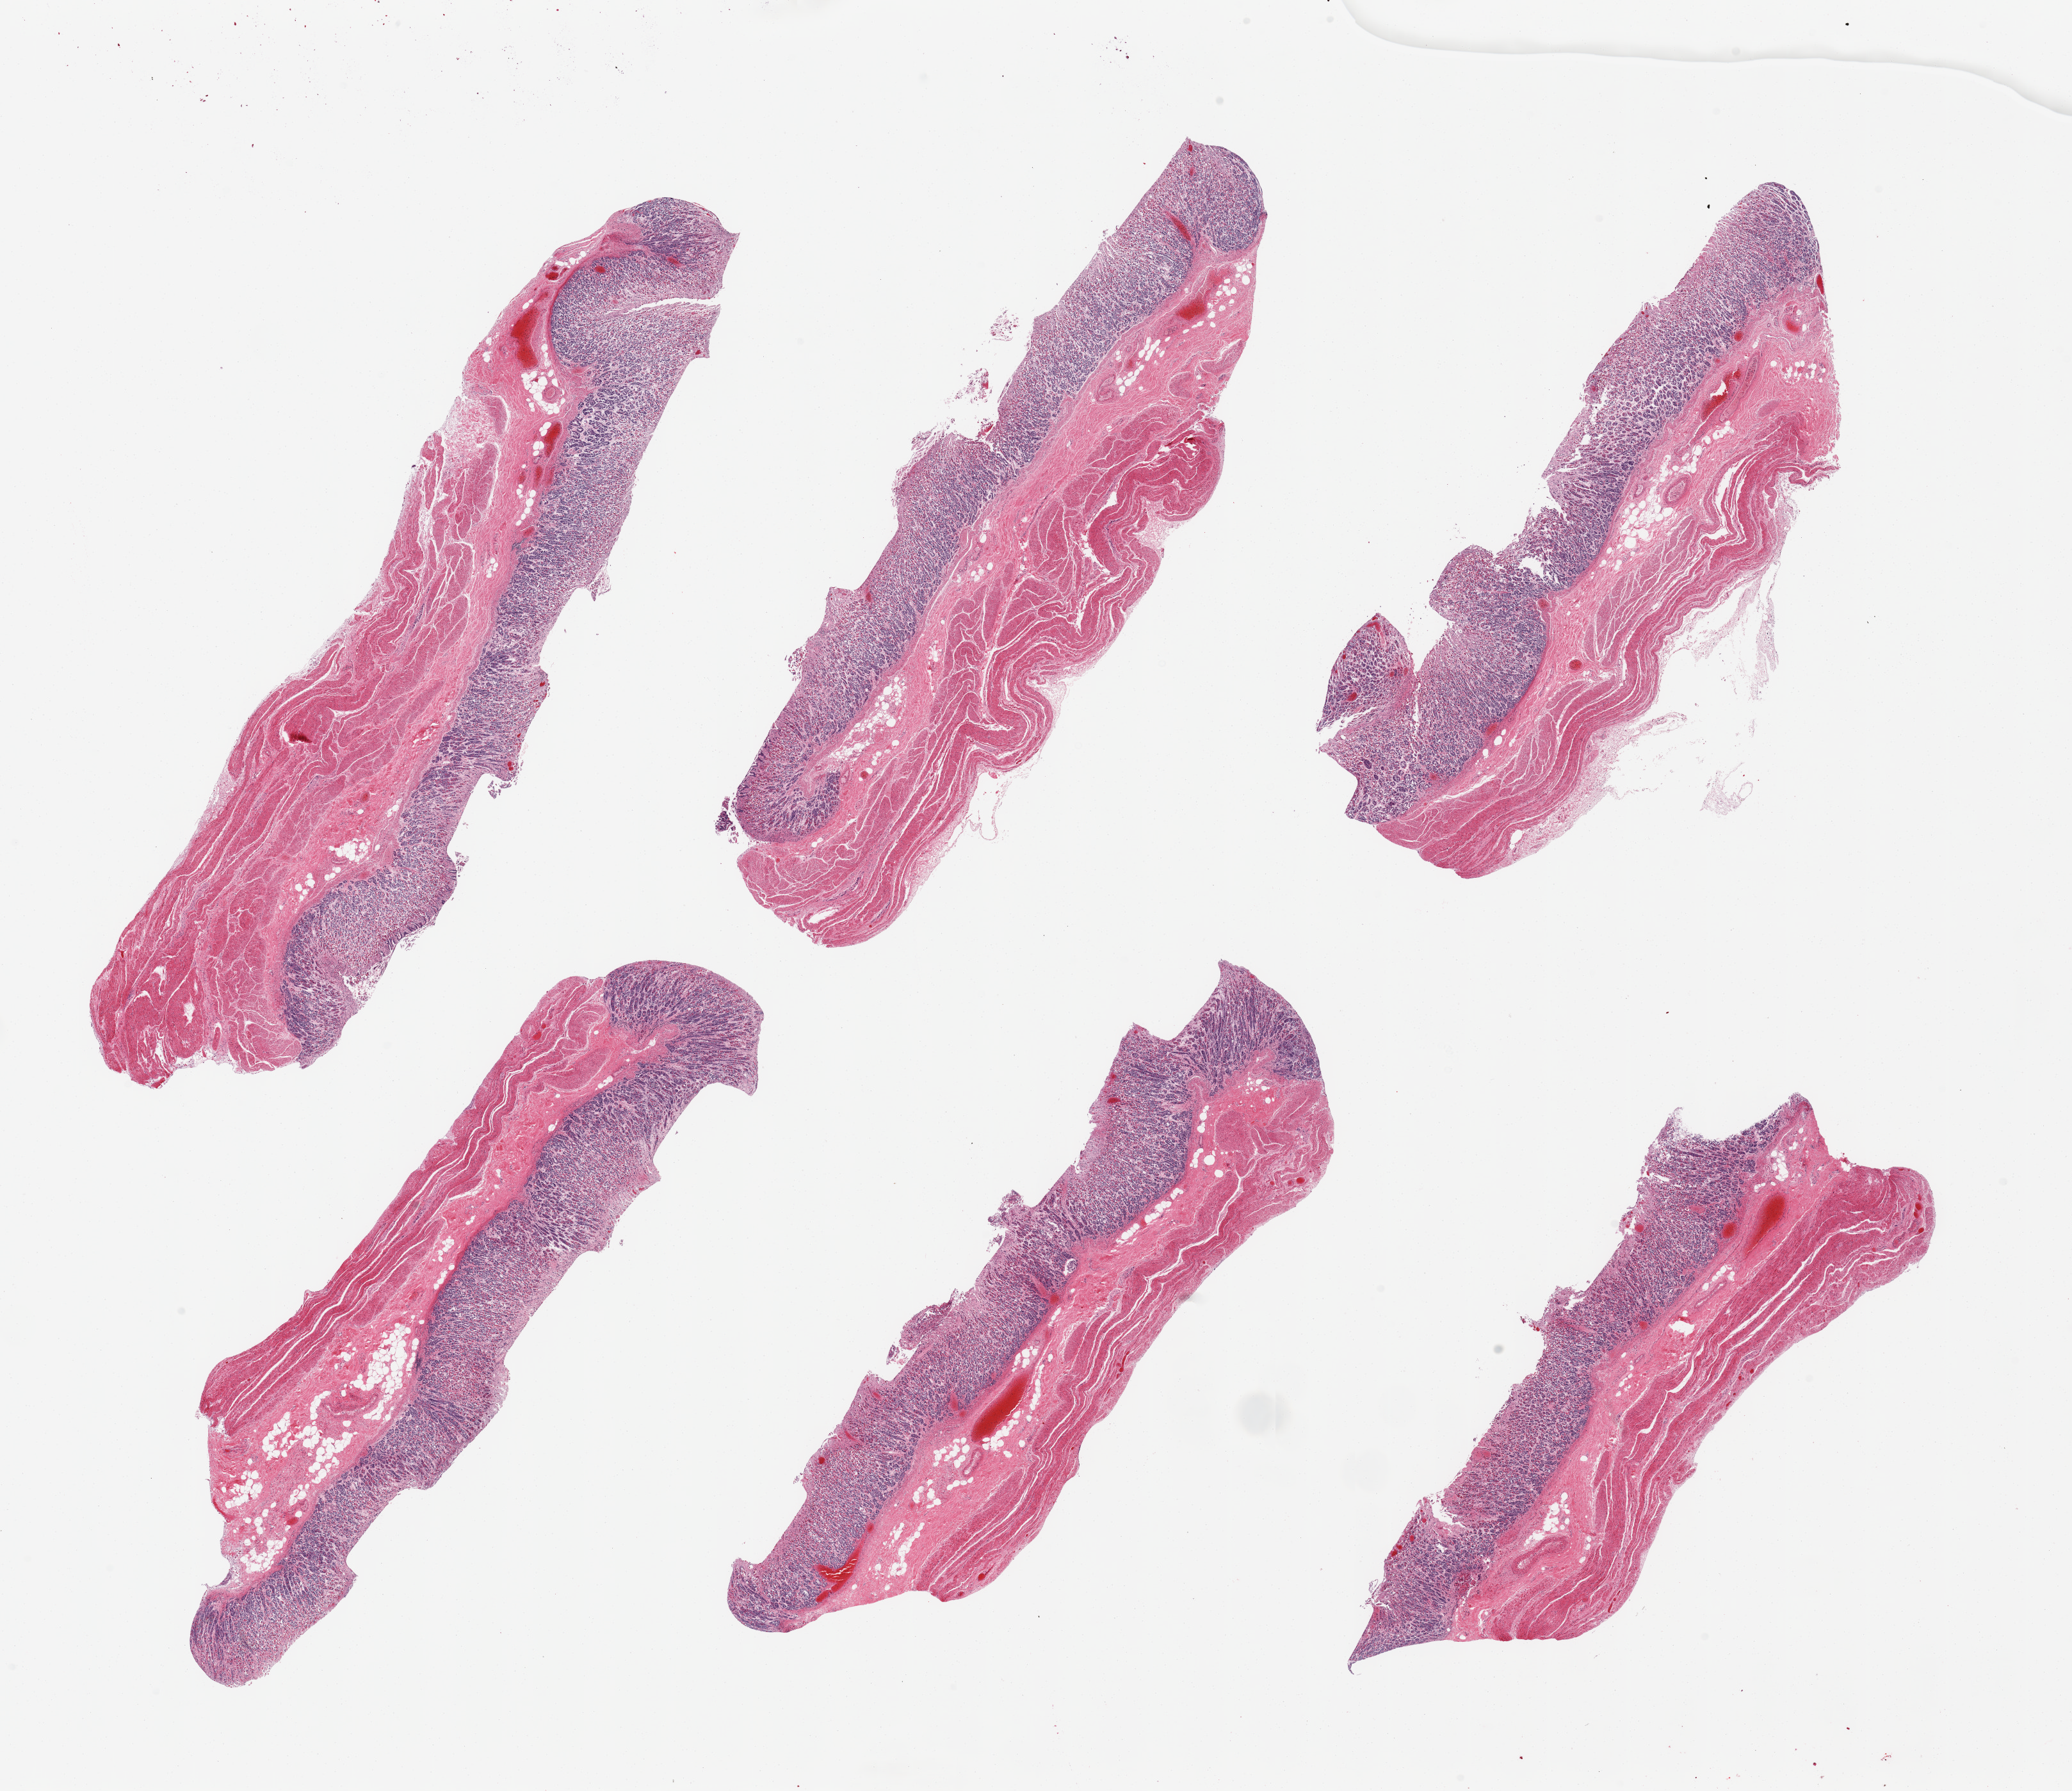
Digitized H&E-stained section — whole scanned area (about 25.6 x 22.1 mm) shown as a low-resolution overview; PAXgene-fixed, paraffin-embedded tissue; section of stomach (target tissue); donor tissue sample. Male donor.
Reviewer comment on this tissue sample: 6 pieces, mucosa up to ~1.2mm, ~50% thickness.